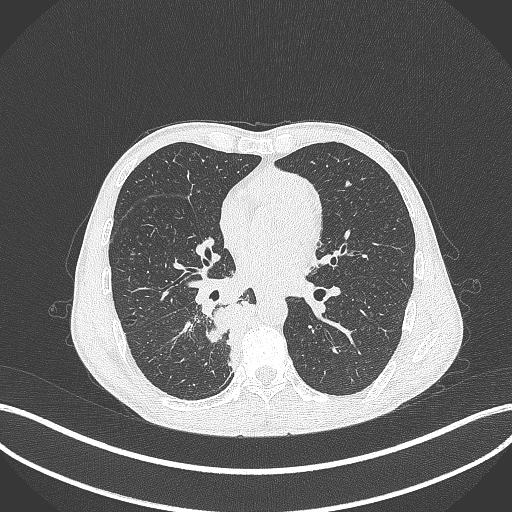
Chest CT, one axial slice. Slice 180 of 371 in the series (ordered by position). Reconstruction kernel B70f. 120 kVp. Lung window (W 1500 / L -600 HU). 1 mm slice thickness. 512 × 512 image matrix. Patient: male, 58 years. From the clinical record (not read from this slice): clinical TNM (as recorded): T3 N1 M1.
Outlined on this slice (bounding box drawn by a radiologist):
- lung tumour (recorded histology: squamous cell carcinoma): box from (x=205, y=299) to (x=258, y=371) px